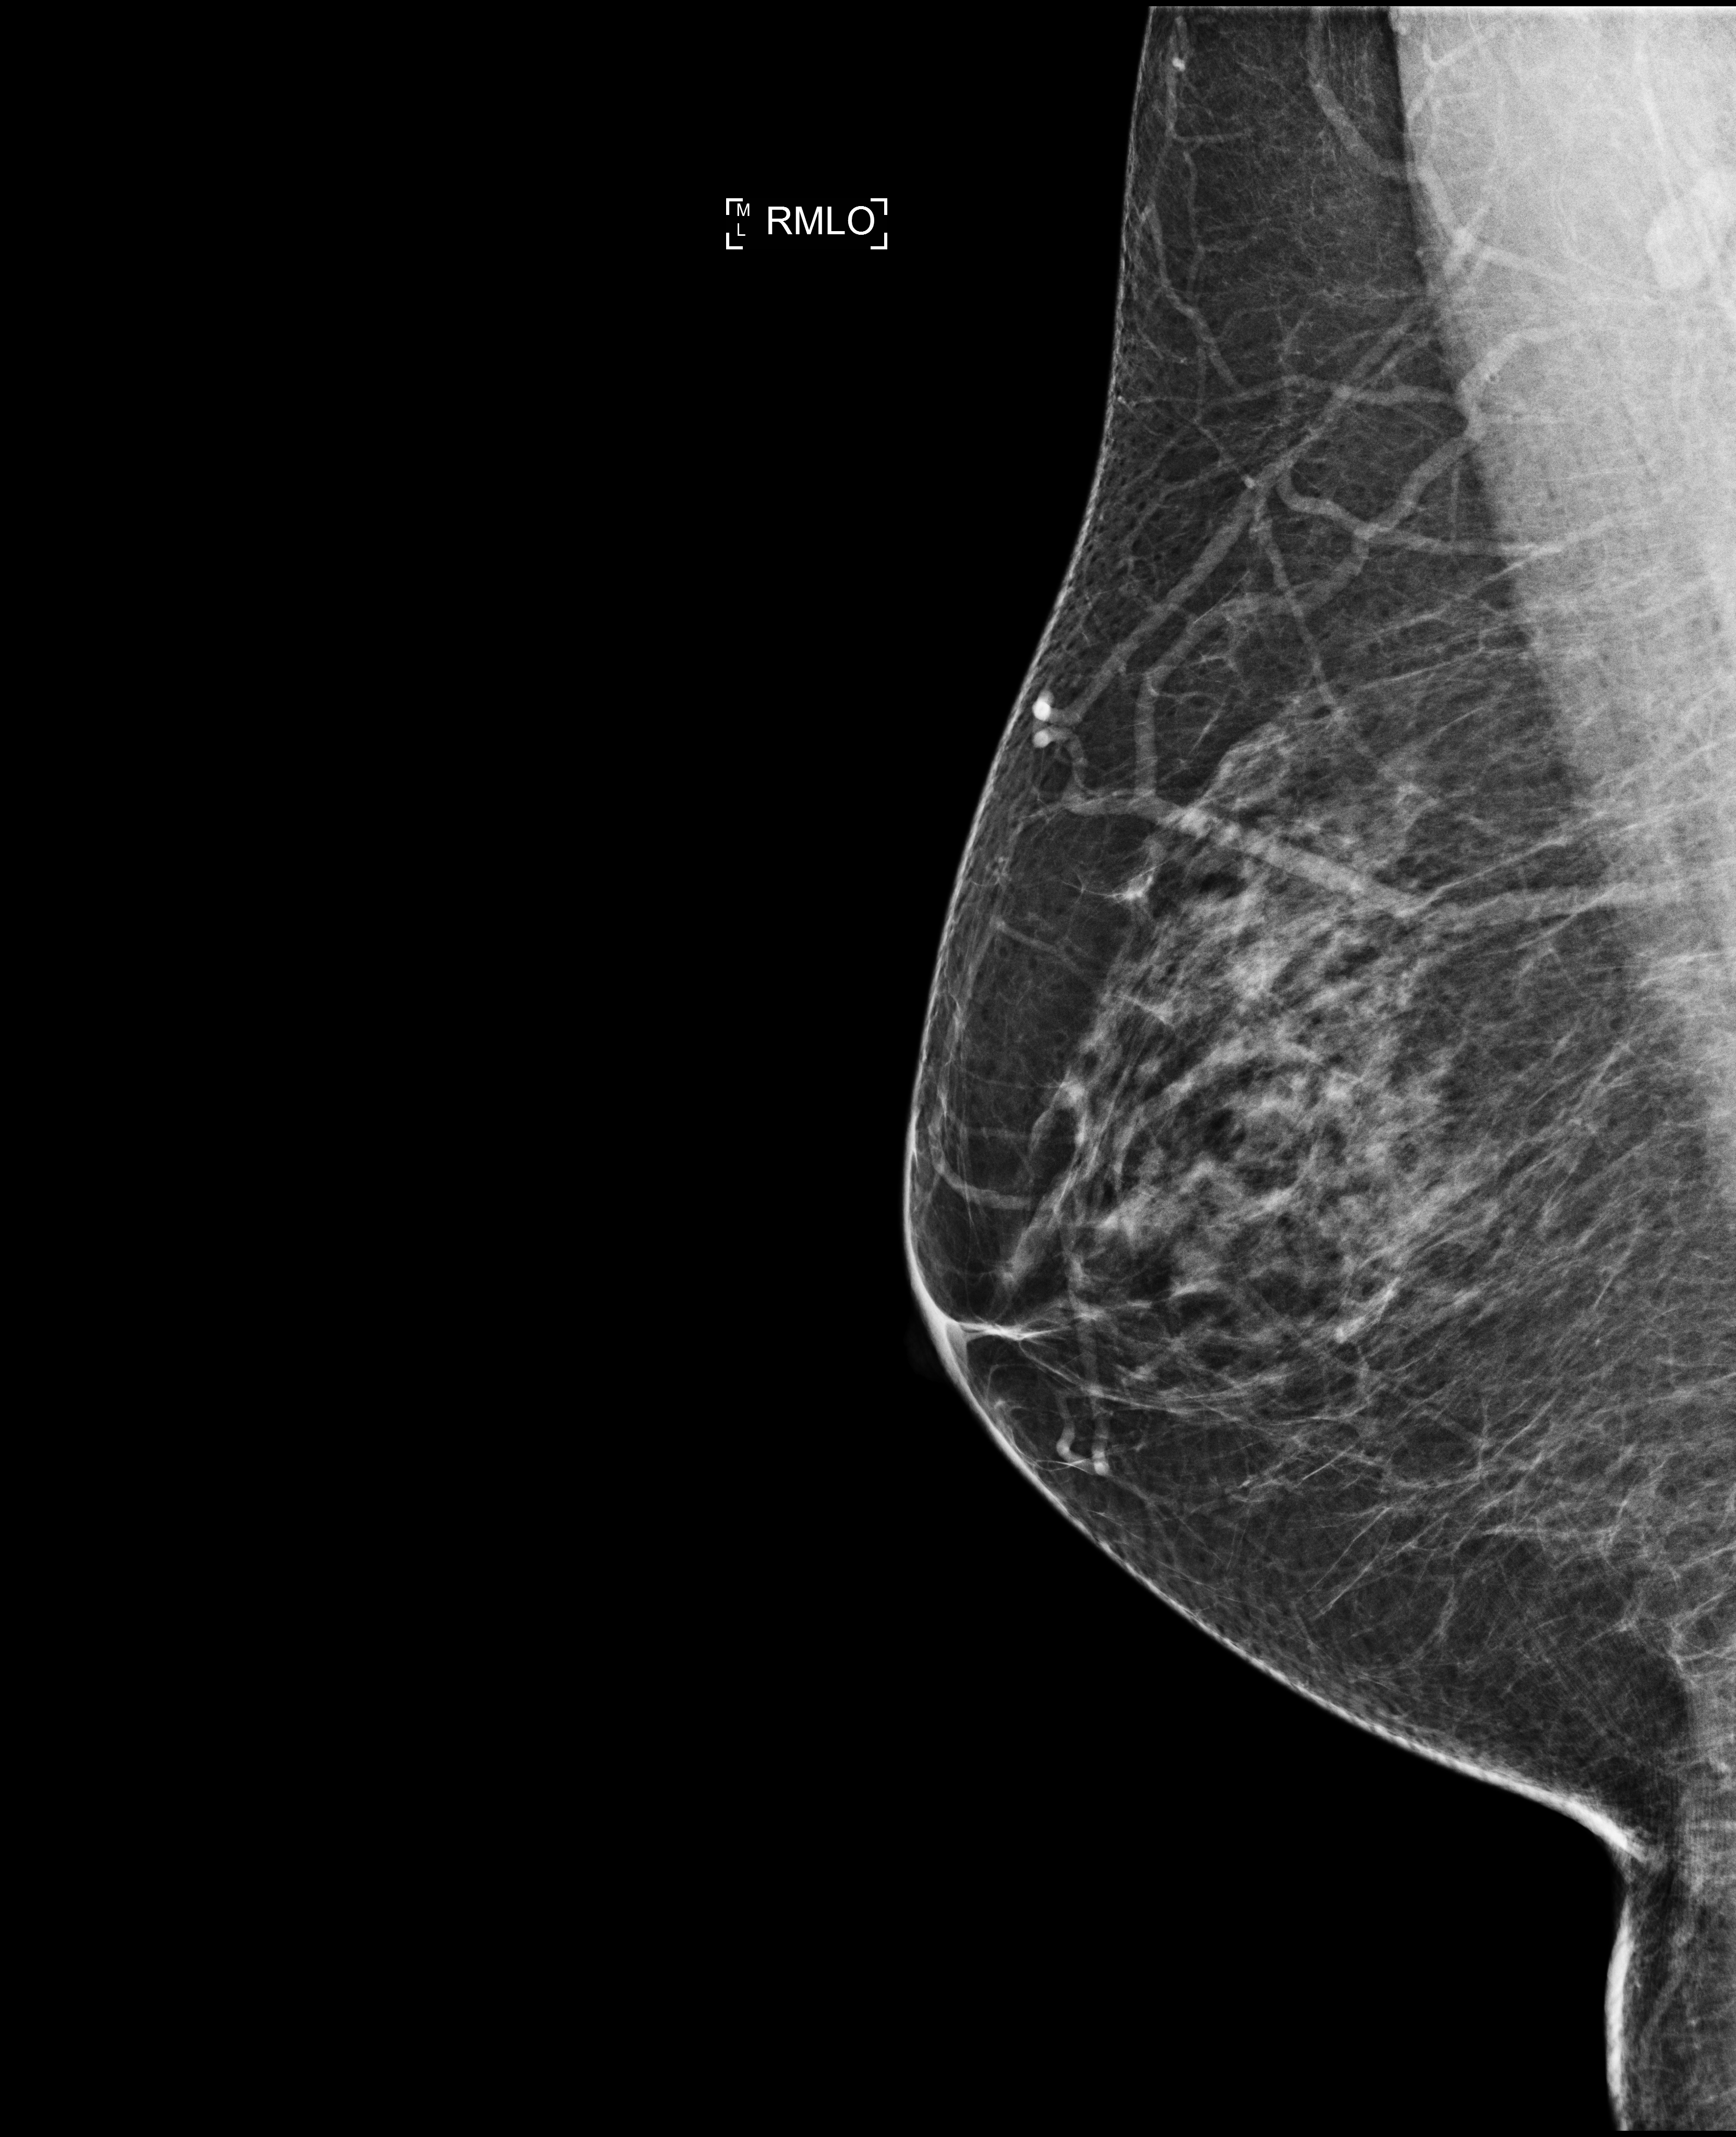
Full-field digital mammogram (FFDM); right breast; medio-lateral oblique projection; screening examination. Female patient, age 56 years.
Final BI-RADS category for the screening round (tomosynthesis exam, both breasts): category 1.